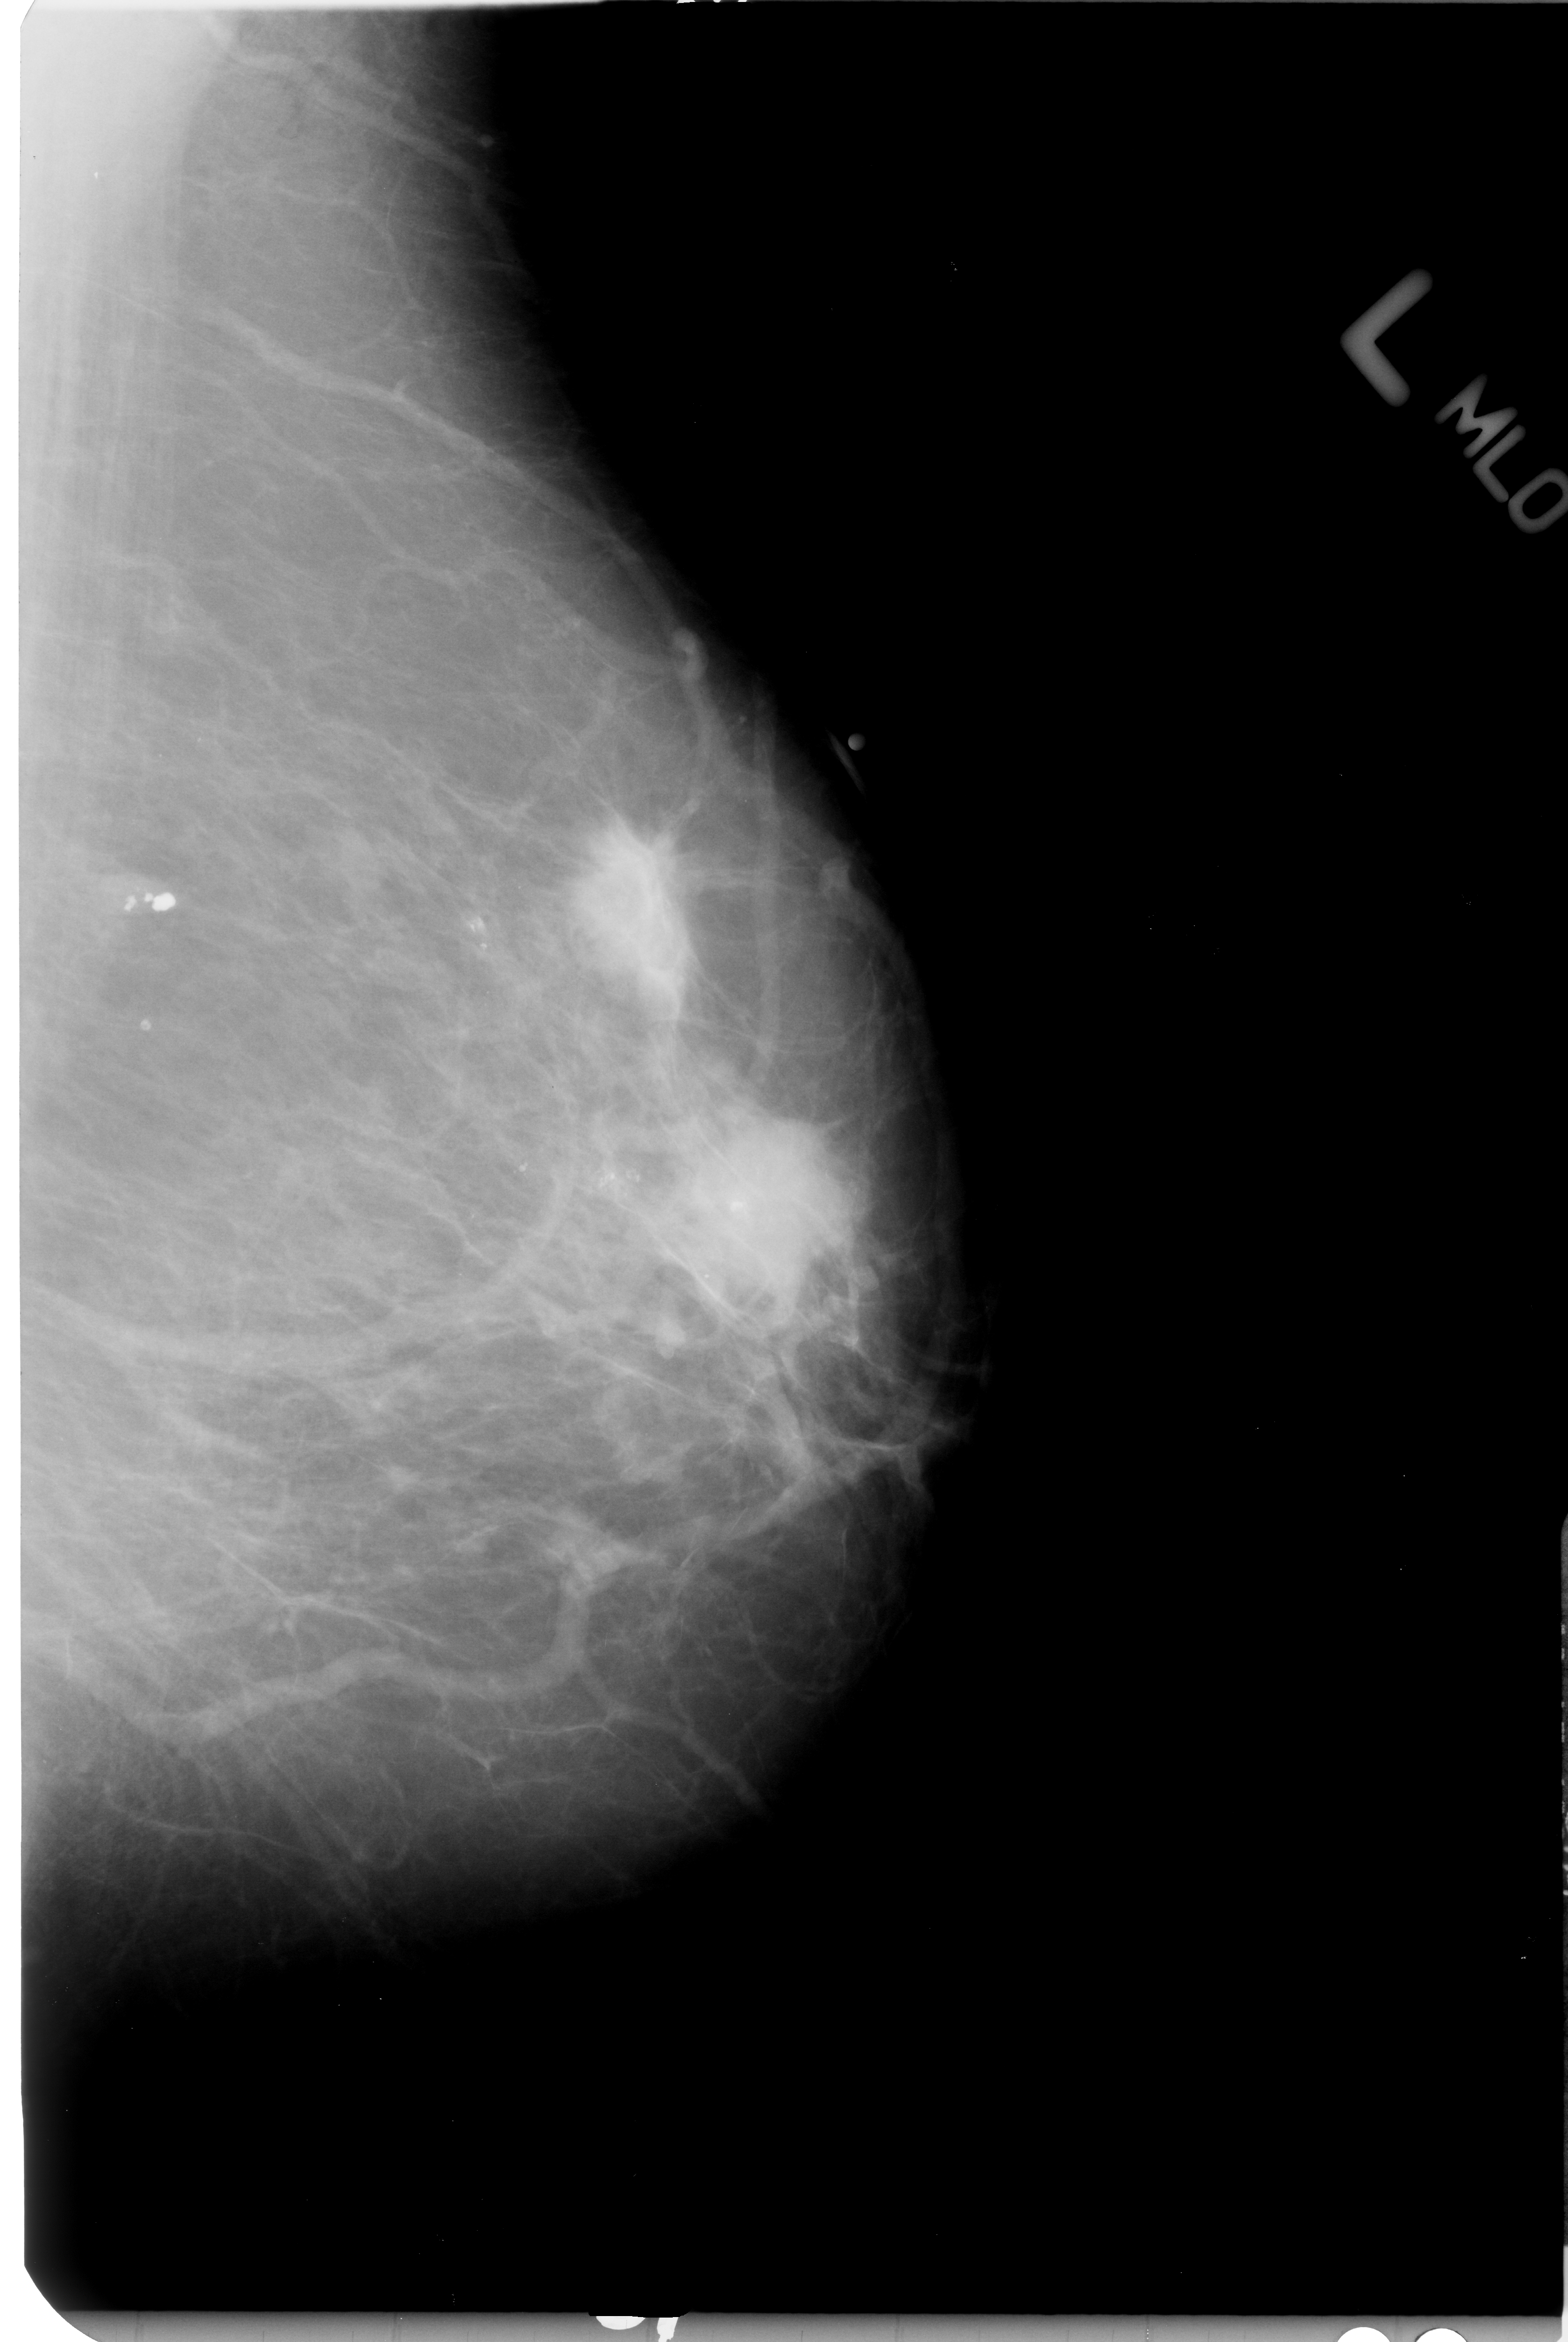
Digitized screen-film mammogram; left breast; mediolateral oblique (MLO) view.
Radiologist-marked abnormalities on this image: Finding 1 of 2: mass, shape irregular / architectural distortion, margins spiculated; BI-RADS assessment category 5; pathology (as recorded): malignant. Finding 2 of 2: mass, shape irregular, margins ill defined / spiculated; BI-RADS assessment category 4; pathology (as recorded): malignant.